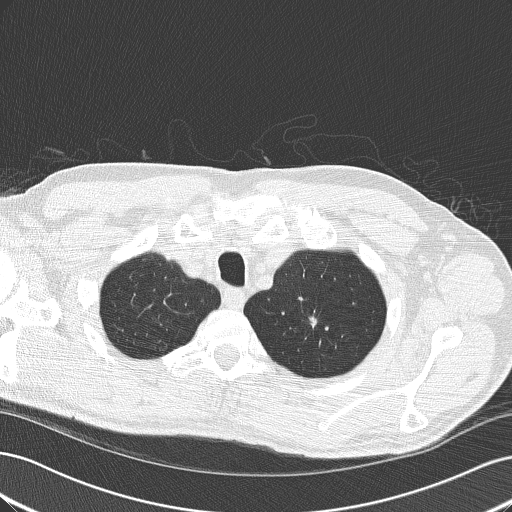
Axial slice from a low-dose chest CT screening exam, third screening round (two years after baseline), lung window (W 1500 / L -600 HU), 2 mm slice thickness, 120 kVp, slice 32 of 192 in the series, 512 × 512 image matrix, field of view 360 × 360 mm. Male participant, aged 64 years at enrolment.
Expert reader's lesion annotation, box from (x=290, y=303) to (x=331, y=342) px. The exam's reader record, not a measurement of the box and not confirmed to be the same lesion: non-calcified nodule or mass ≥4 mm, left upper lobe, 8 × 8 mm, smooth margins, soft tissue attenuation, pre-existing on the prior screen: yes; interval growth: yes. Lung cancer was diagnosed 111 days after this screen: adenocarcinoma, NOS, left upper lobe, poorly differentiated (G3), stage IA (AJCC 6th edition), 10 mm at pathology.